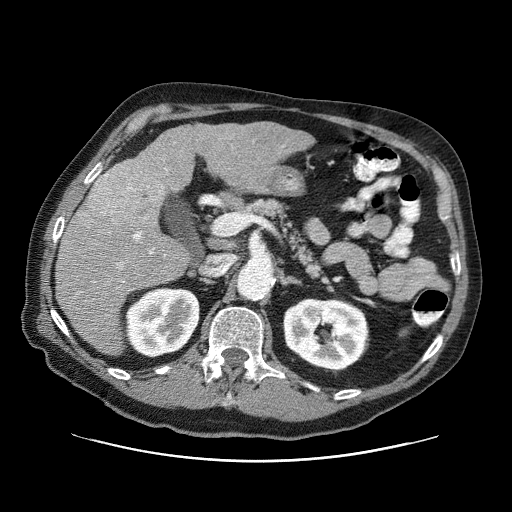
Contrast-enhanced abdominal CT (liver protocol), one axial slice. Slice 35 of 87 in the series (ordered by position). Reconstruction kernel STANDARD. One of 3 acquisitions stored at this slice position. Soft-tissue window (W 400 / L 40 HU). 512 × 512 image matrix, field of view 400 × 400 mm. Case-level facts recorded for this patient, not image findings: diagnosis: hepatocellular carcinoma (patient treated with transarterial chemoembolisation; whether this scan precedes or follows treatment is not stated here); TNM stage (as recorded): Stage-IIIA; Child-Pugh class: A; tumour differentiation: well differentiated; tumour size: 6 cm.
Annotated regions visible in this slice (semi-automatic segmentation, software-assisted and operator-edited):
- liver parenchyma outside the tumour (the mass and vessels are separate outlines, so this box may not span the whole liver): bounding box <56,122,314,354> (left, top, right, bottom; pixels)
- mass: <86,155,165,229>
- liver vessels: <78,232,154,294>